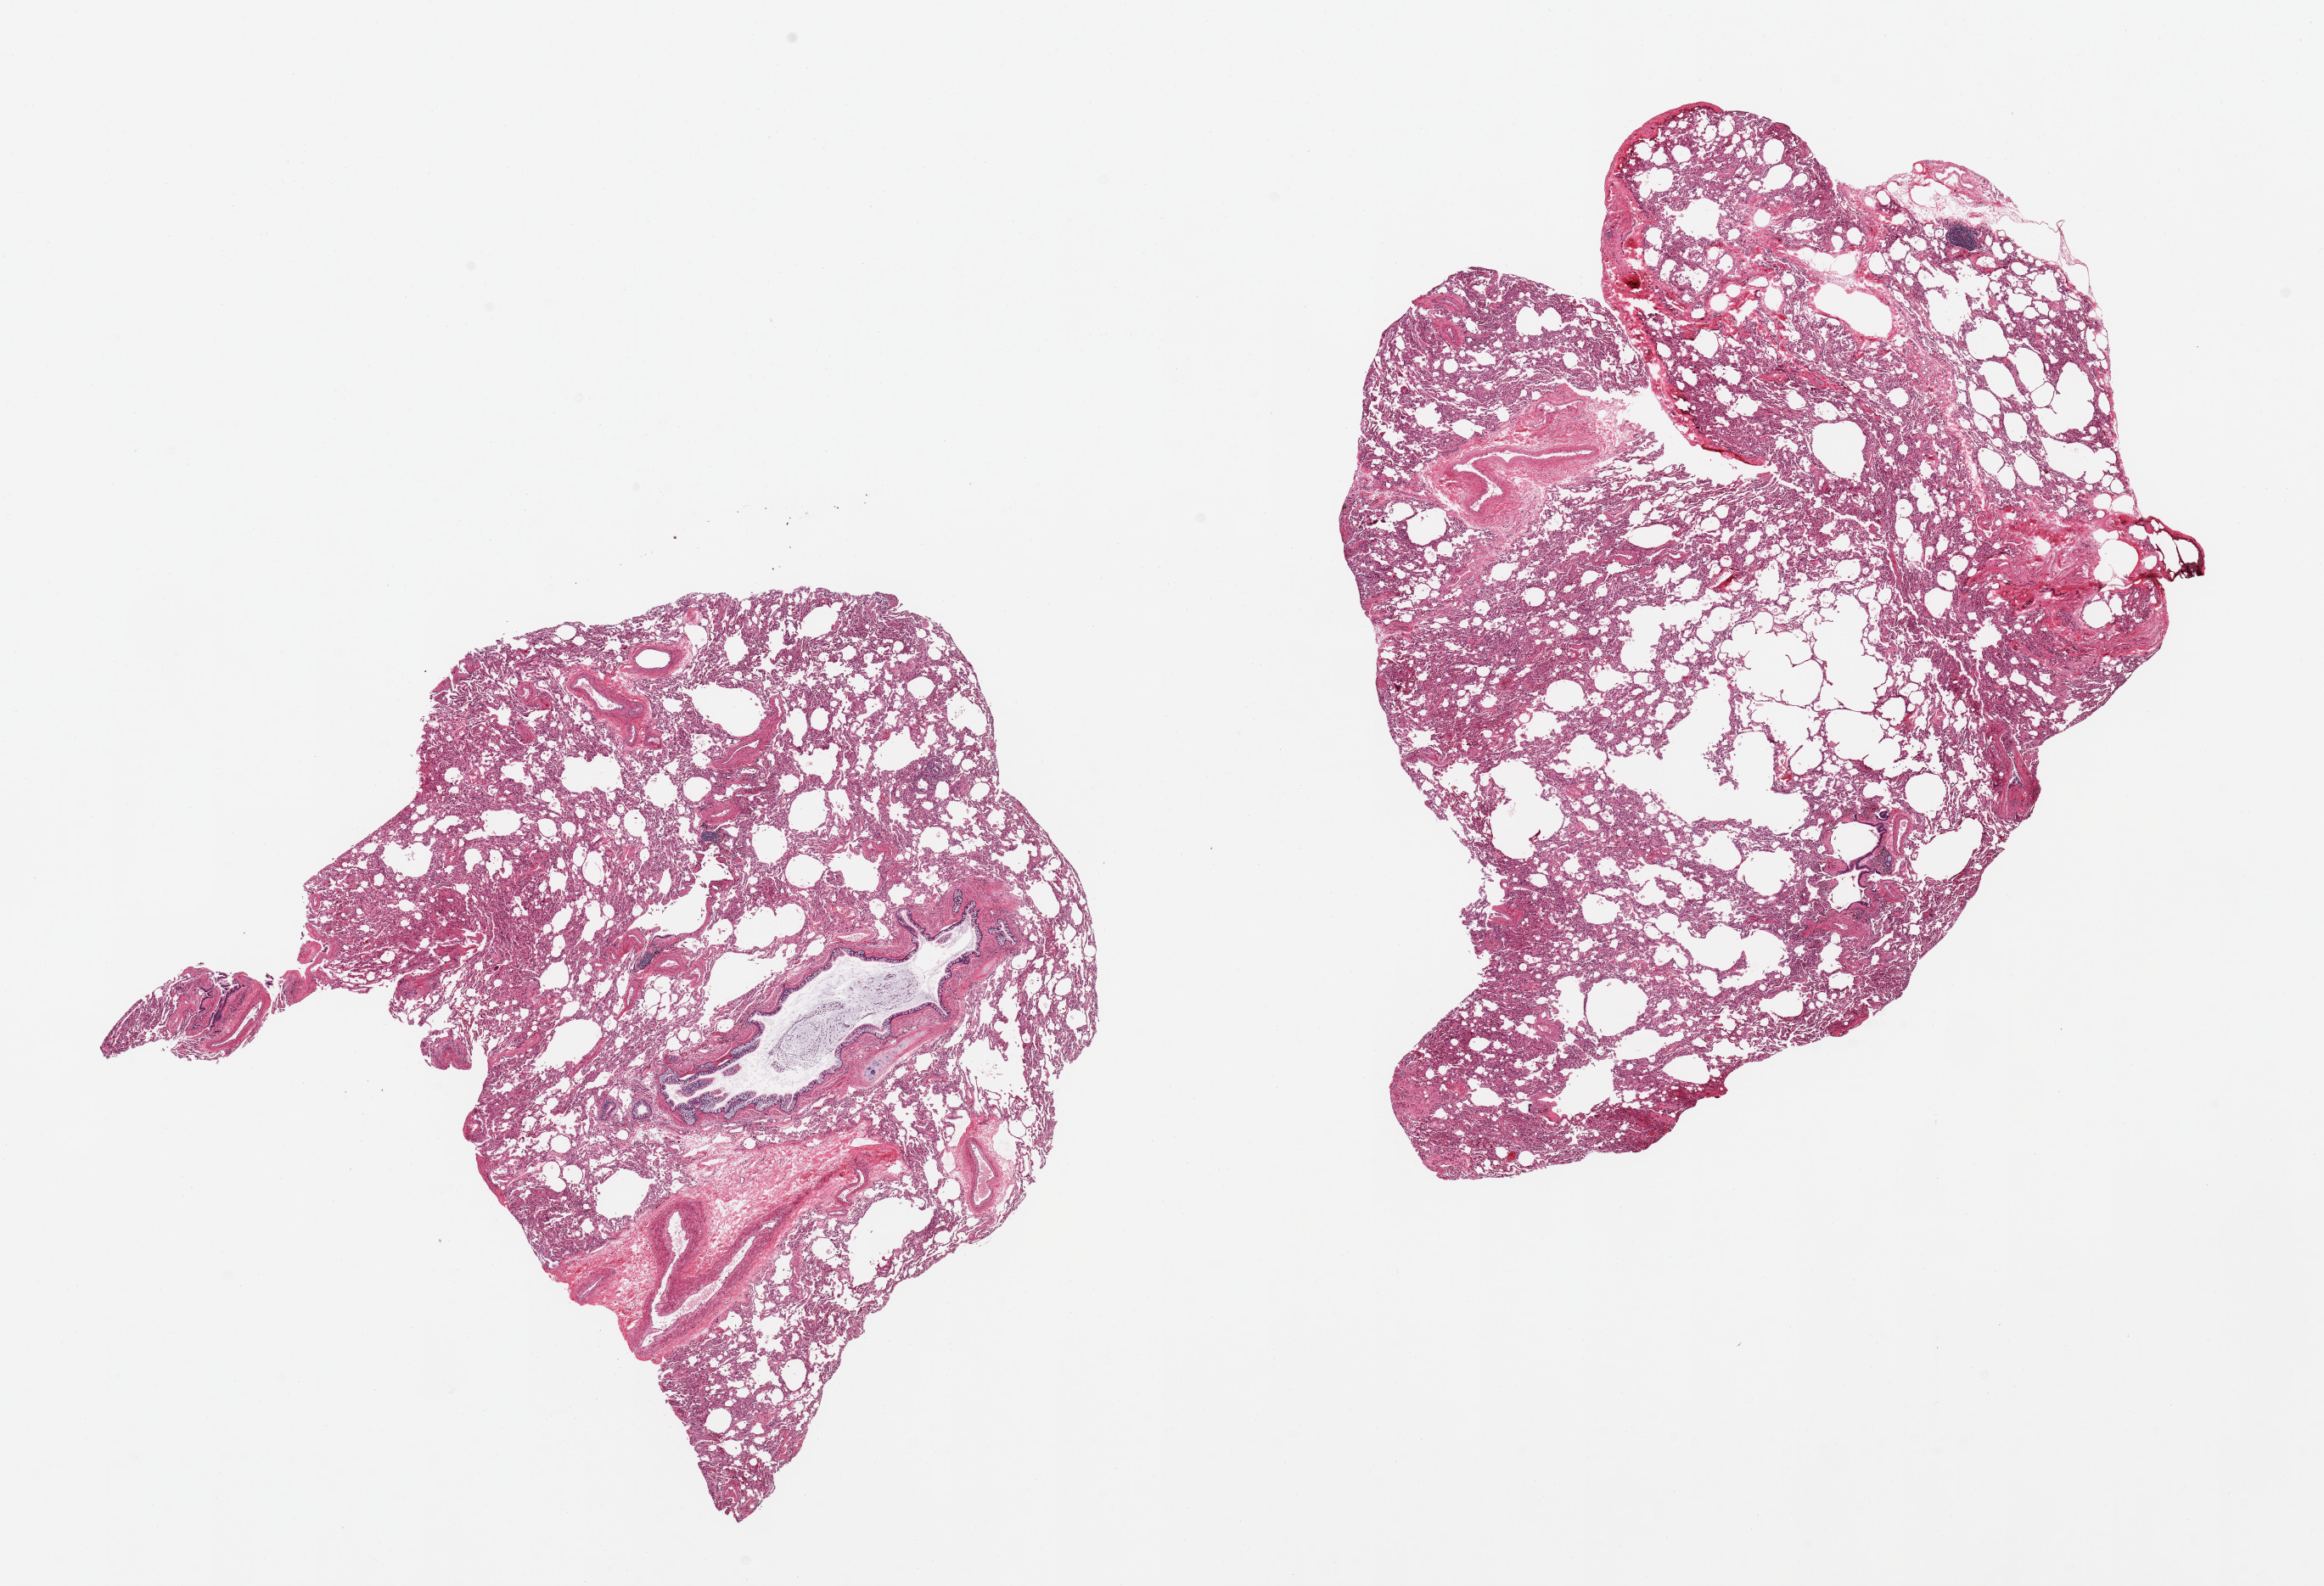
Hematoxylin and eosin (H&E) whole-slide image, brightfield, shown as a low-resolution overview of the whole scanned area (about 21.7 x 14.8 mm, acquisition: 20x scan); PAXgene-fixed, paraffin-embedded tissue; section of lung (target tissue); tissue donor sample. Male donor.
Review note (as recorded): 2 pieces; mild mucopurulent exudate in bronchus.